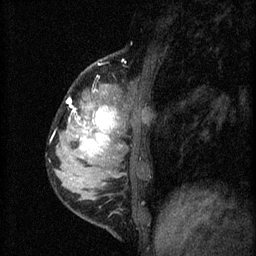
Breast MRI (dynamic contrast-enhanced), one sagittal slice. 3 images stored at this slice position (order not interpretable as contrast timing). 1.5 T. TE 4.2 ms, TR 8.2 ms. 2 mm slice thickness. 256 × 256 image matrix, field of view 180 × 180 mm. Patient: female, 37 years.
Outlined on this slice (semi-automatically segmented with operator editing):
- analysis volume of interest (the breast-tissue region the enhancement analysis was run in; not a lesion): bounding box (x1, y1, x2, y2) in pixels: (54, 78, 140, 181)
- tumour enhancement mask (voxels above the 70 % enhancement threshold inside the analysis volume of interest): (68, 100, 118, 157)